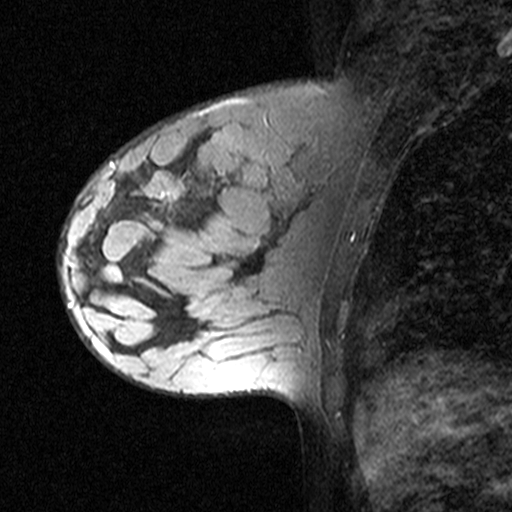
Breast MRI (dynamic contrast-enhanced), one sagittal slice. Position 15 of 44 along the scan axis. Dynamic contrast-enhanced study with each time point stored as its own series, time point 2 of 3 at this slice position (early post-contrast, ordered by acquisition time). 1.5 T. TE 4.5 ms, TR 11 ms. 3 mm slice thickness. 512 × 512 image matrix, field of view 200 × 200 mm. Patient: female, 27 years. Case-level facts recorded for this patient, not image findings: setting: breast cancer imaged before/during neoadjuvant chemotherapy; receptor status: HR-positive, HER2-negative.
Structures marked on this image (semi-automatically segmented with operator editing):
- analysis volume of interest (the breast-tissue region the enhancement analysis was run in; not a lesion): box from (x=59, y=162) to (x=163, y=271) px
- tumour enhancement mask (voxels above the 90 % enhancement threshold inside the analysis volume of interest): (x=80, y=162)–(x=135, y=248)